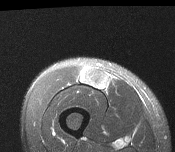
MRI of an extremity soft-tissue mass, one axial slice; position 44 of 116 along the scan axis; T2-weighted fat-saturated; MR volume resampled by the dataset authors to the PET/CT grid (not the native acquisition matrix); 3.27 mm slice thickness; 175 × 152 image matrix, field of view 171 × 148 mm. Male patient. From the clinical record (not read from this slice): histological type: pleiomorphic leiomyosarcoma; grade: intermediate; site of the primary tumour: right thigh.
Outlined on this slice (expert contour drawn on MRI and transferred to this co-registered scan by the dataset authors):
- gross tumour volume including surrounding oedema: bounding box <81,68,109,89> (left, top, right, bottom; pixels)